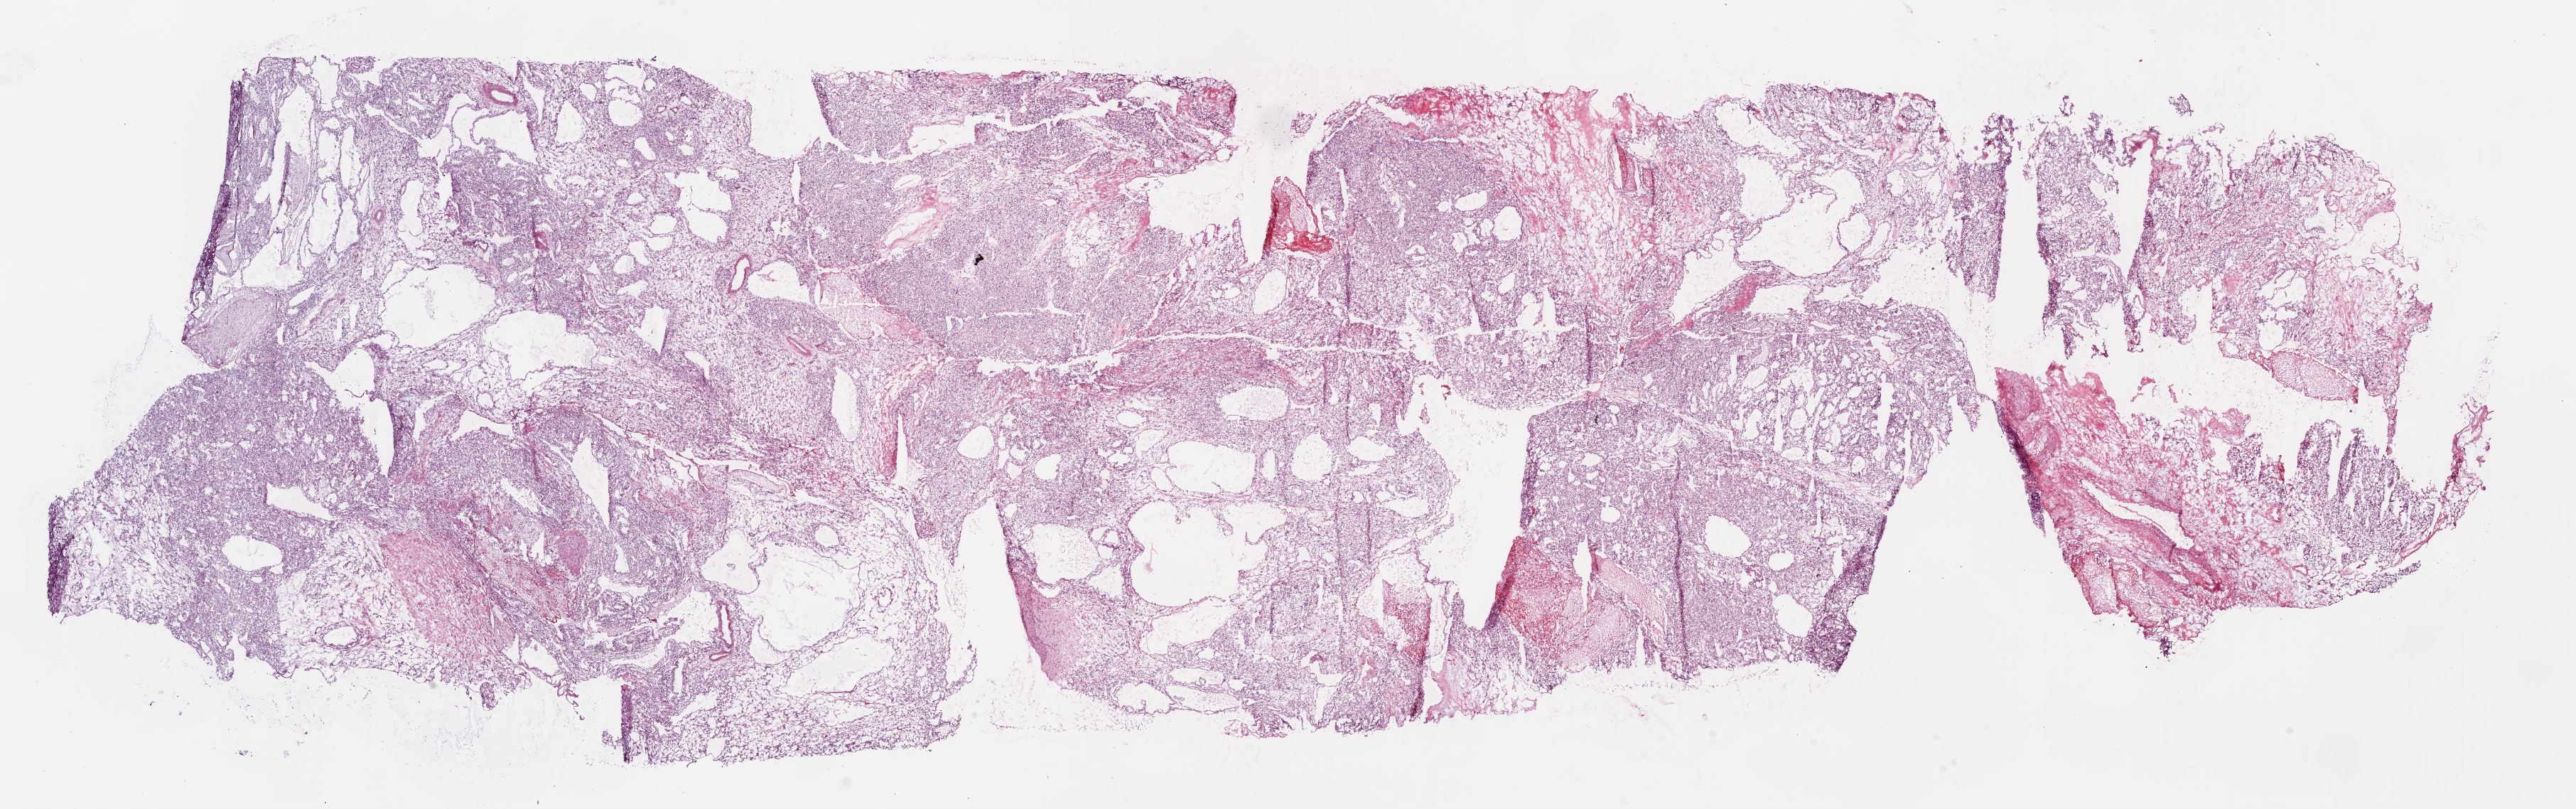
Whole-slide histology image, H&E-stained, shown as a low-resolution overview of the whole scanned area (about 29.1 x 9.1 mm). Frozen section. Kidney, primary tumour sample. Male, age 47 years at initial diagnosis. Histologic grade: G2 (moderately differentiated). Slide review estimates, as recorded: tumour cells 90%, tumour nuclei 85%, normal cells 0%, stromal cells 10%, necrosis 0%.
AJCC pathologic stage: II (7th edition). Histologic diagnosis: Clear cell adenocarcinoma, NOS.